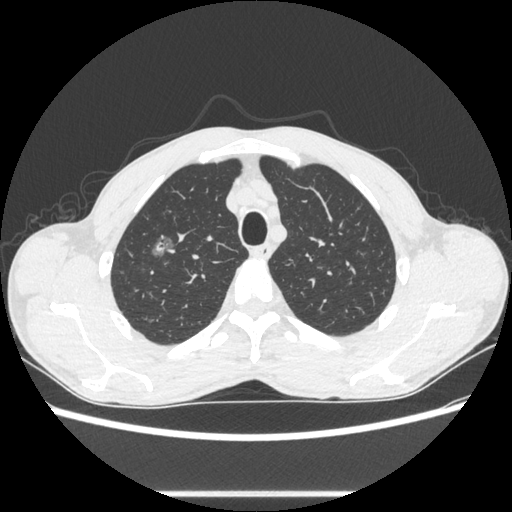
Chest CT, one axial slice; slice 482 of 600 in the series (ordered by position); reconstruction kernel STANDARD; lung window (W 1500 / L -600 HU); 0.62 mm slice thickness; 512 × 512 image matrix. Male patient, age 54 years. From the clinical record (not read from this slice): clinical TNM (as recorded): T1a N0 M0.
Structures marked on this image (bounding box drawn by a radiologist):
- lung tumour (recorded histology: adenocarcinoma): bounding box (x1, y1, x2, y2) in pixels: (145, 224, 178, 263)